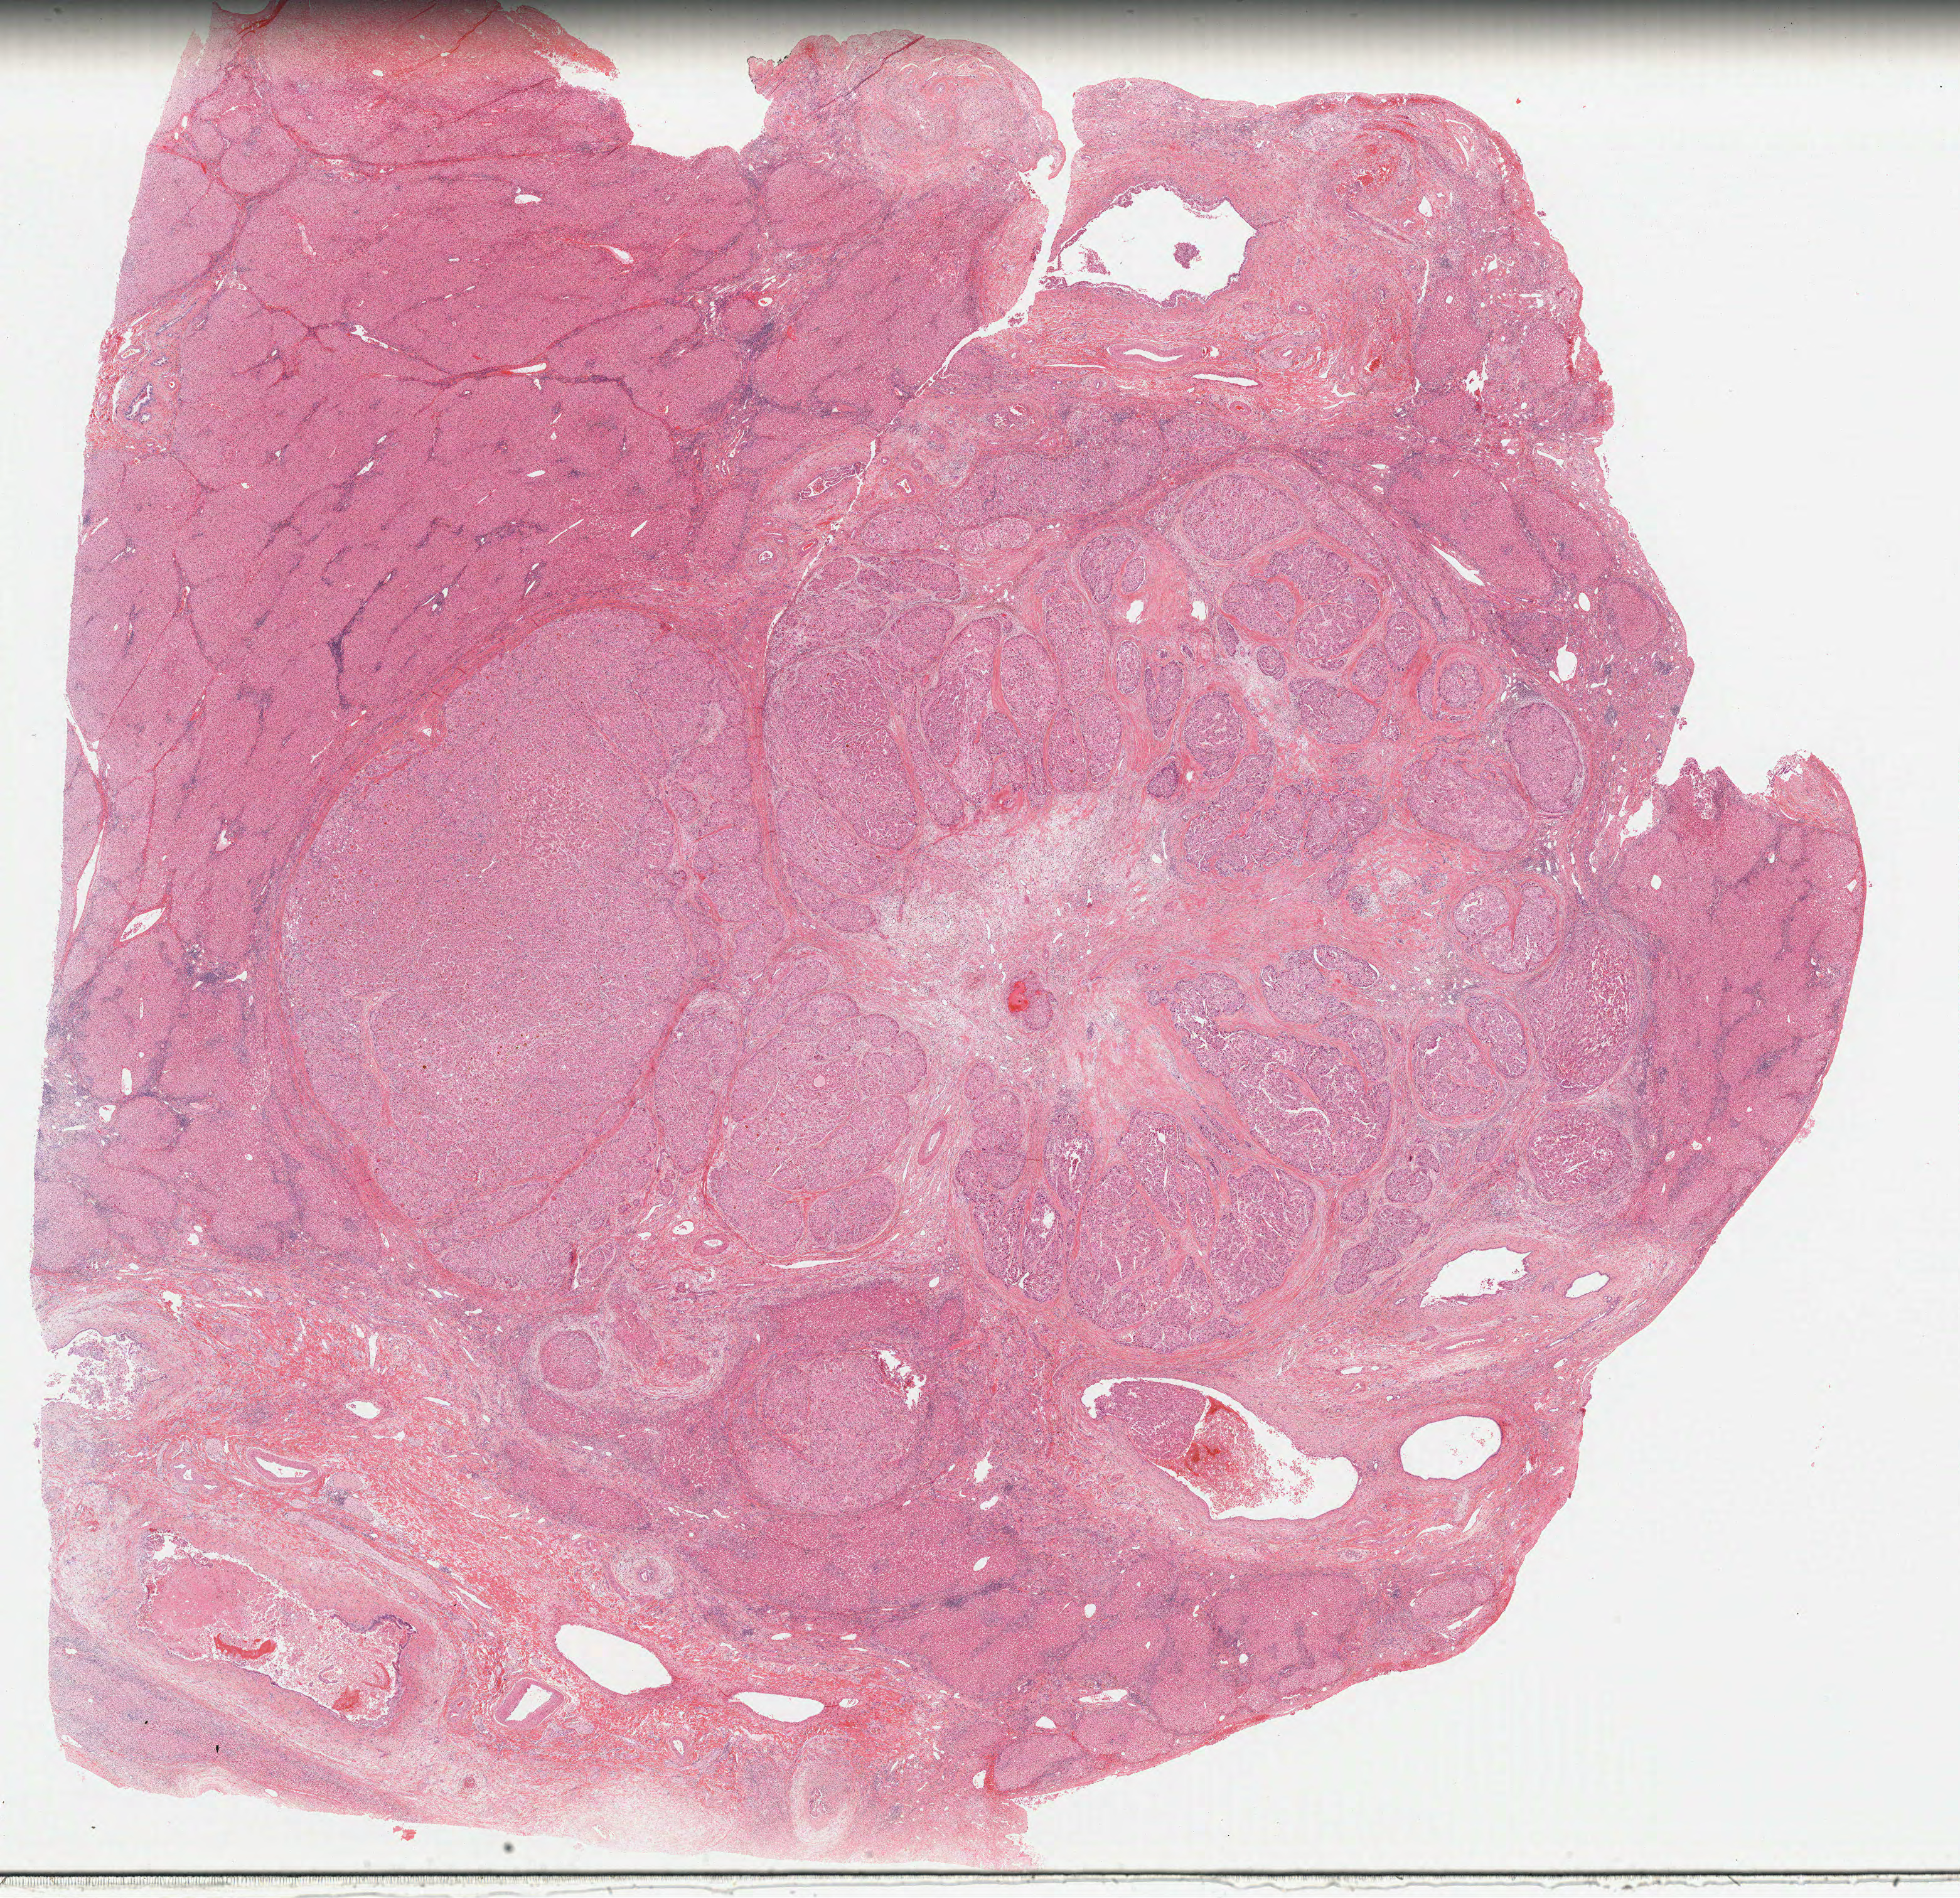
Whole-slide histology image, H&E, shown as a low-resolution overview of the whole scanned area (about 24.7 x 23.9 mm, from a 40x scan). Formalin-fixed paraffin-embedded (FFPE) diagnostic section. Sample: primary tumour, liver. Male patient; age at initial diagnosis 35 years. Histologic grade: G2 (moderately differentiated).
* TNM: T1 N0 M0
* AJCC pathologic stage: I (6th edition)
* diagnosis: Hepatocellular carcinoma, NOS